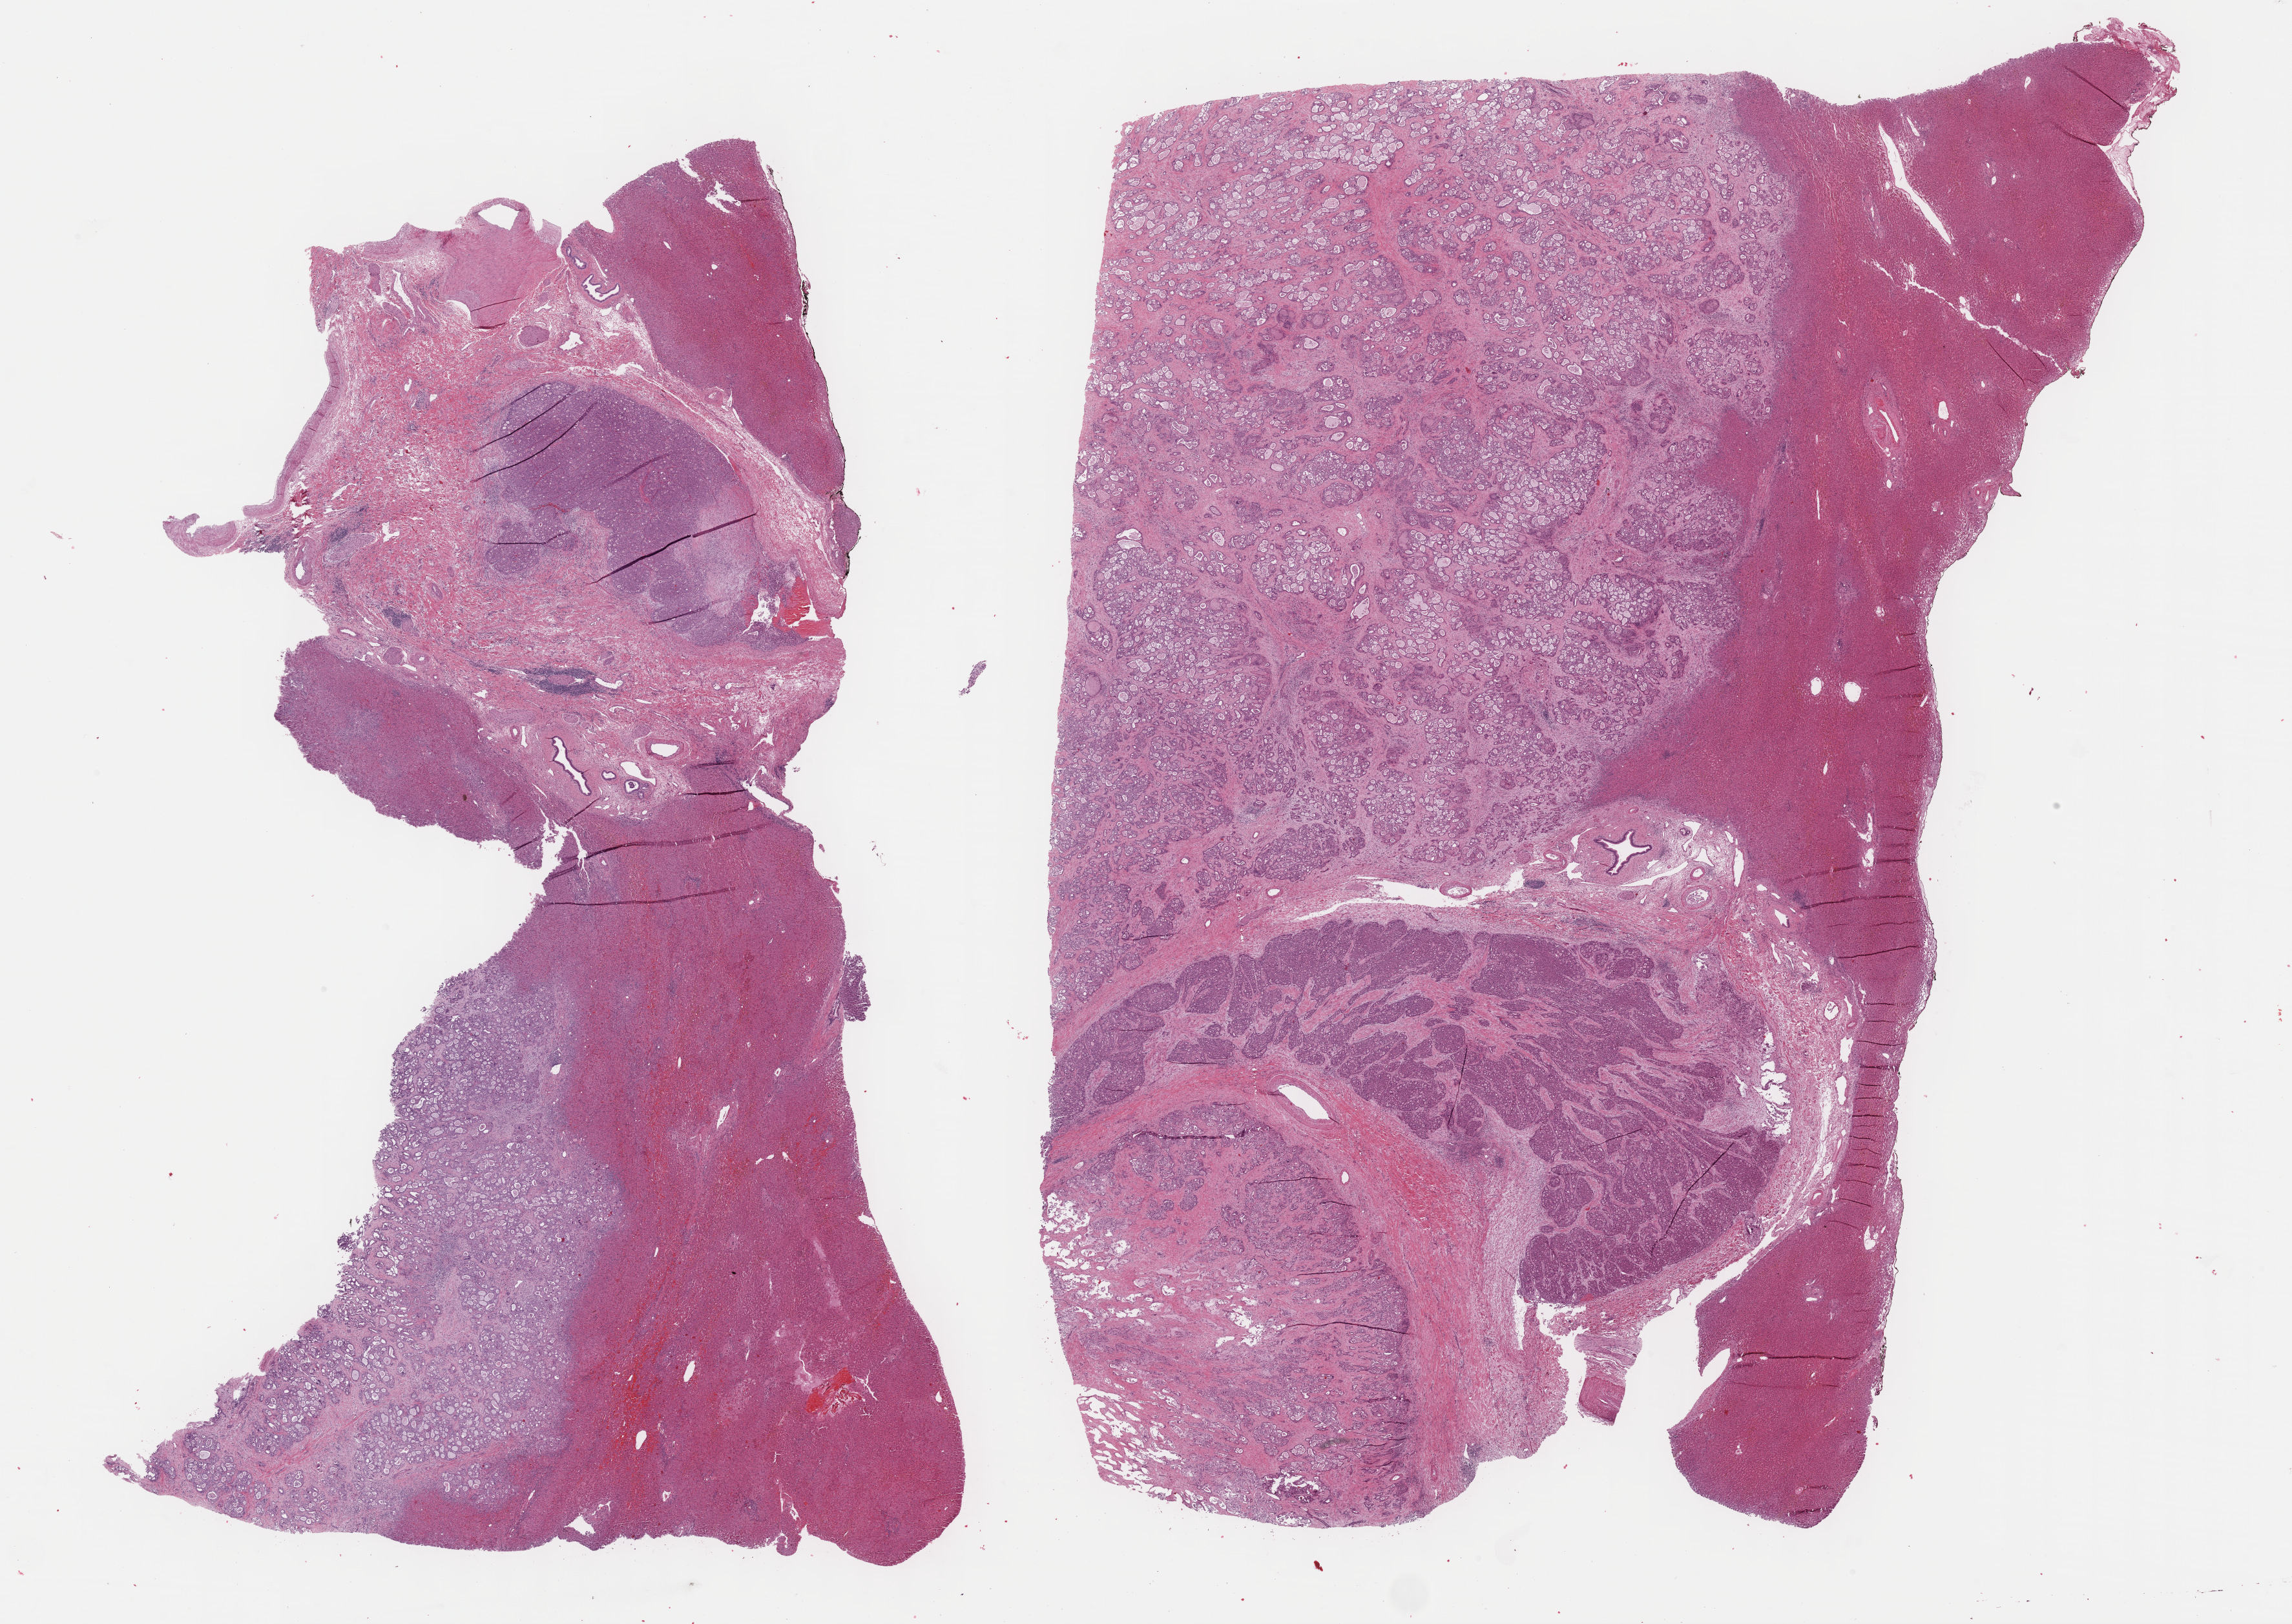
Whole-slide histology image, Hematoxylin and eosin (H&E) stained — shown as a low-resolution overview of the whole scanned area (about 28.7 x 20.3 mm). Formalin-fixed paraffin-embedded (FFPE) diagnostic section. Primary tumour sample from the bile duct. Female patient; age at initial diagnosis 78 years.
Diagnosis: Cholangiocarcinoma (intrahepatic bile duct).